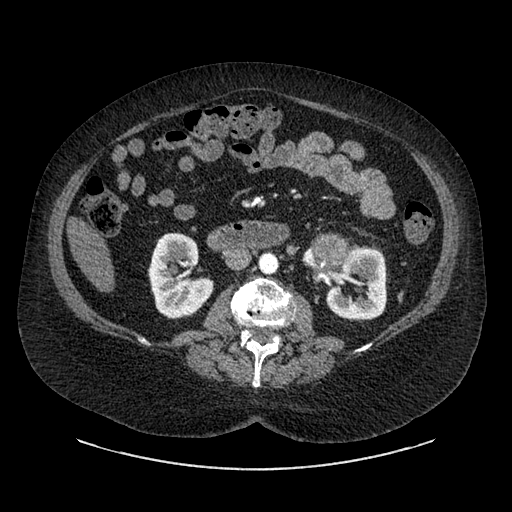
Contrast-enhanced abdominal CT, one axial slice. Slice 487 of 769 in the series (ordered by position). Reconstruction kernel SOFT. Intravenous contrast given. Soft-tissue window (W 400 / L 40 HU). 512 × 512 image matrix, field of view 460 × 460 mm. Patient: female, 61 years. From the clinical record (not read from this slice): diagnosis: adrenocortical carcinoma; tumour side: left adrenal; tumour size at pathology: 13 cm; Ki-67 index: 79 %; stage (as recorded): 2.
Structures marked on this image (semi-automatic segmentation, software-assisted and operator-edited):
- mass: box from (x=321, y=239) to (x=343, y=265) px